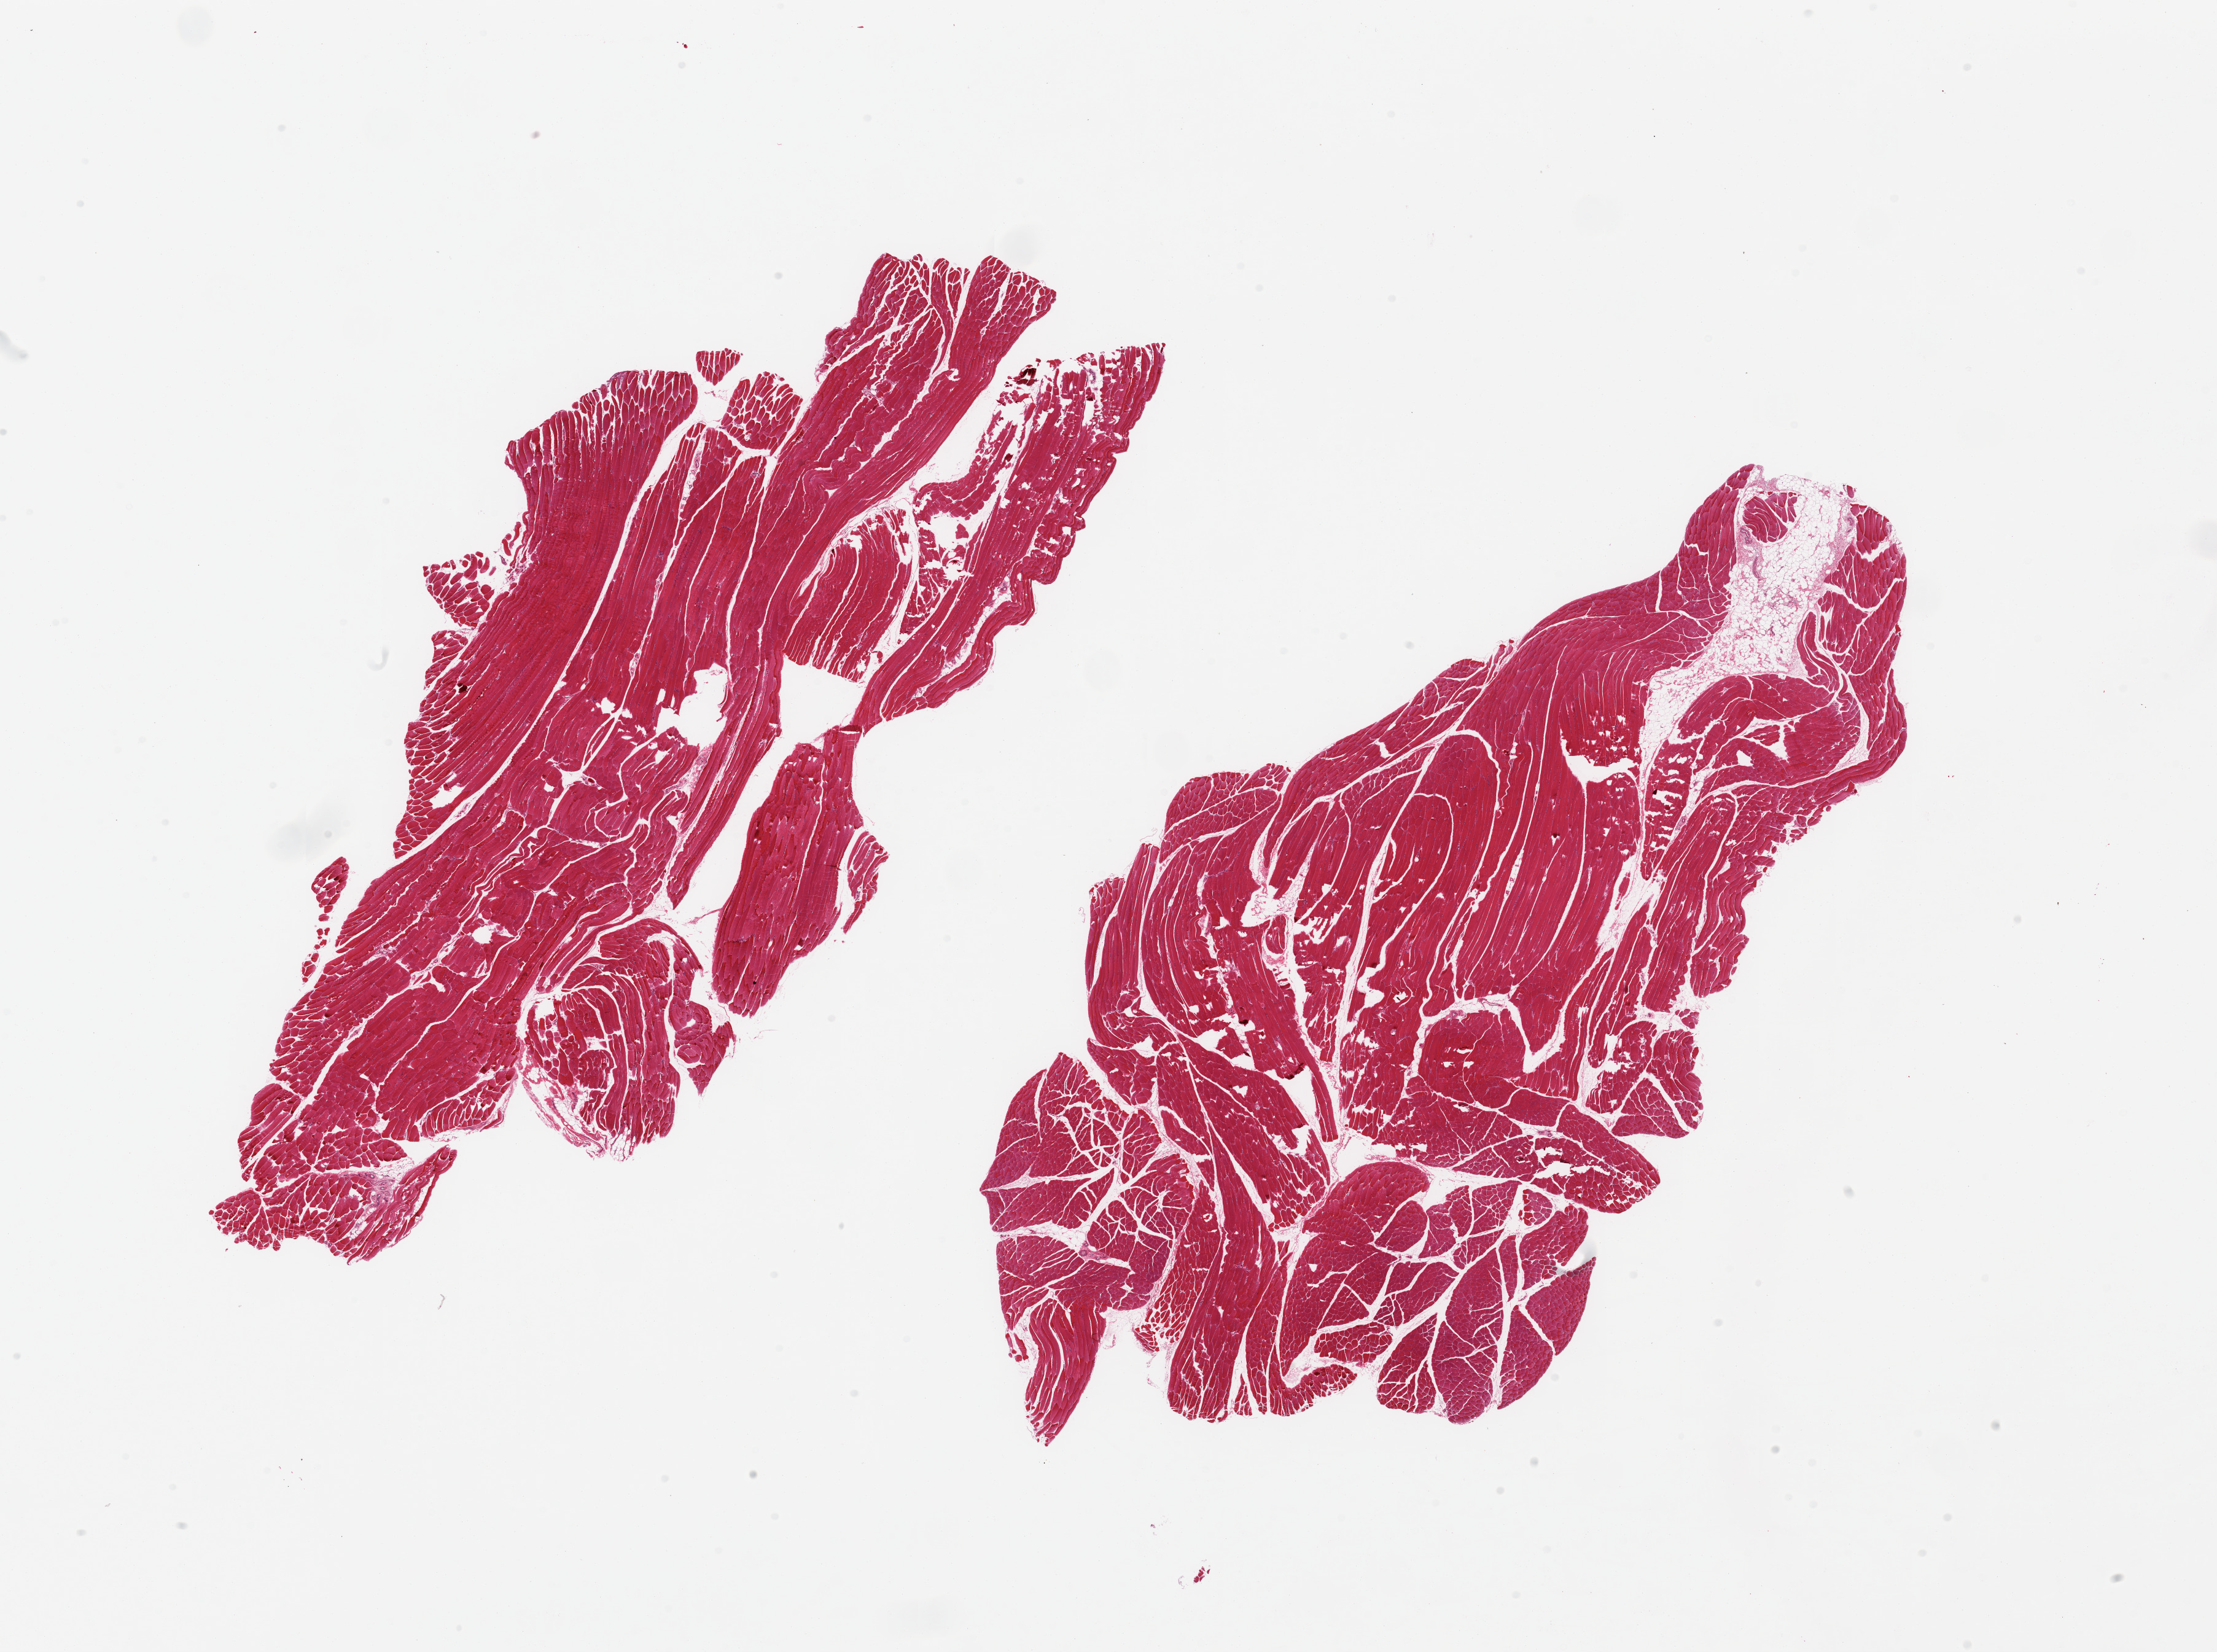
Whole-slide image, haematoxylin and eosin stain — low-resolution overview of the scanned area, about 28.5 x 21.3 mm; PAXgene-fixed paraffin-embedded (PFPE) section; sampled site (target tissue): skeletal muscle; donor tissue sample. Donor sex: male.
Reviewer comment on this tissue sample: 2 pieces, interstitial fat is ~10% of tissue.